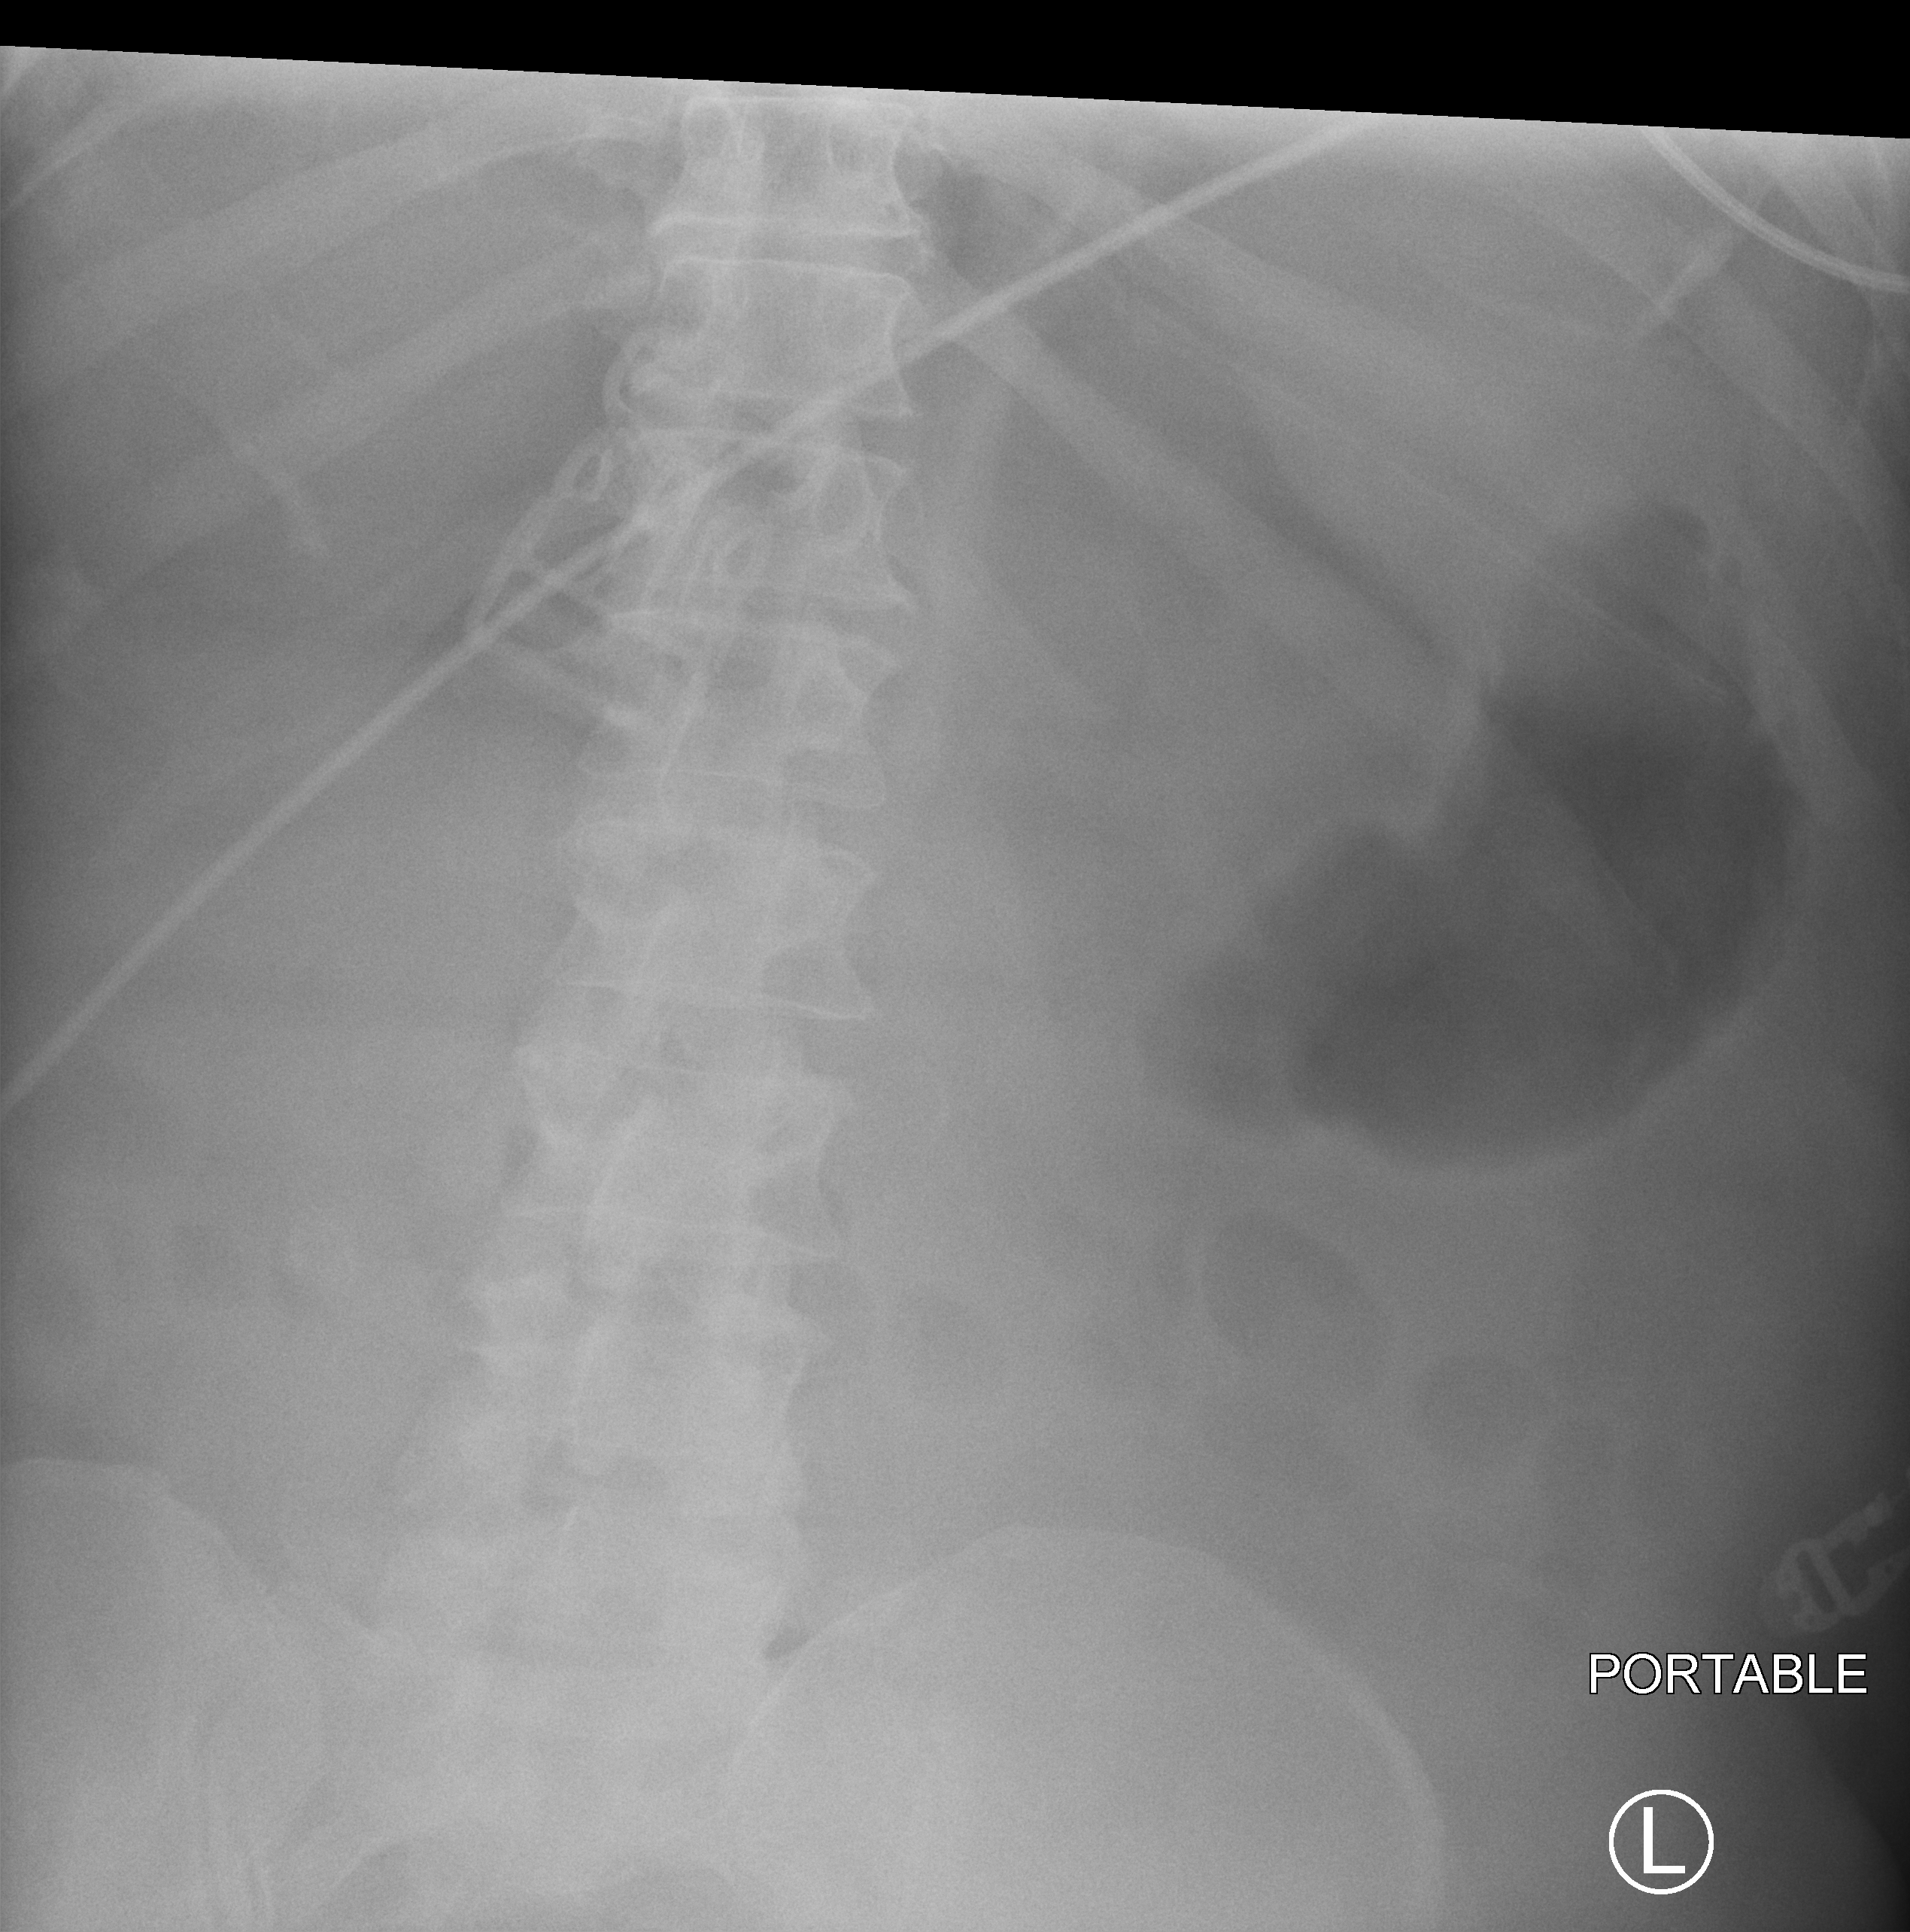
Bedside abdomen radiograph (computed radiography); anteroposterior (AP) projection. Adult patient hospitalised with COVID-19, age 18–59 years.
From the hospital-stay record, not from the radiograph (when in the stay this image was taken is not recorded):
- admitted to intensive care during this hospital stay: yes
- mechanically ventilated during this hospital stay: yes